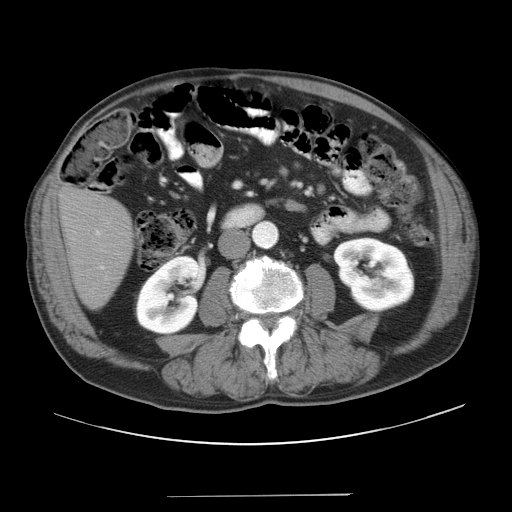
Contrast-enhanced abdominal CT, one axial slice; slice 5 of 41 in the series (ordered by position); 120 kVp; intravenous contrast given; soft-tissue window (W 400 / L 40 HU); 5 mm slice thickness; 512 × 512 image matrix, field of view 420 × 420 mm. Male patient, age 75 years. Case-level facts recorded for this patient, not image findings: diagnosis: colorectal cancer liver metastases, imaged before liver resection; multiple liver metastases: no; largest metastasis: 5.2 cm; disease in both lobes: no.
Structures marked on this image (expert manual segmentation):
- liver: box from (x=60, y=190) to (x=133, y=309) px
- planned liver remnant (the part of the liver to remain after resection): (x=60, y=190)–(x=133, y=309)
- portal vein (with intrahepatic branches): (x=96, y=230)–(x=104, y=269)